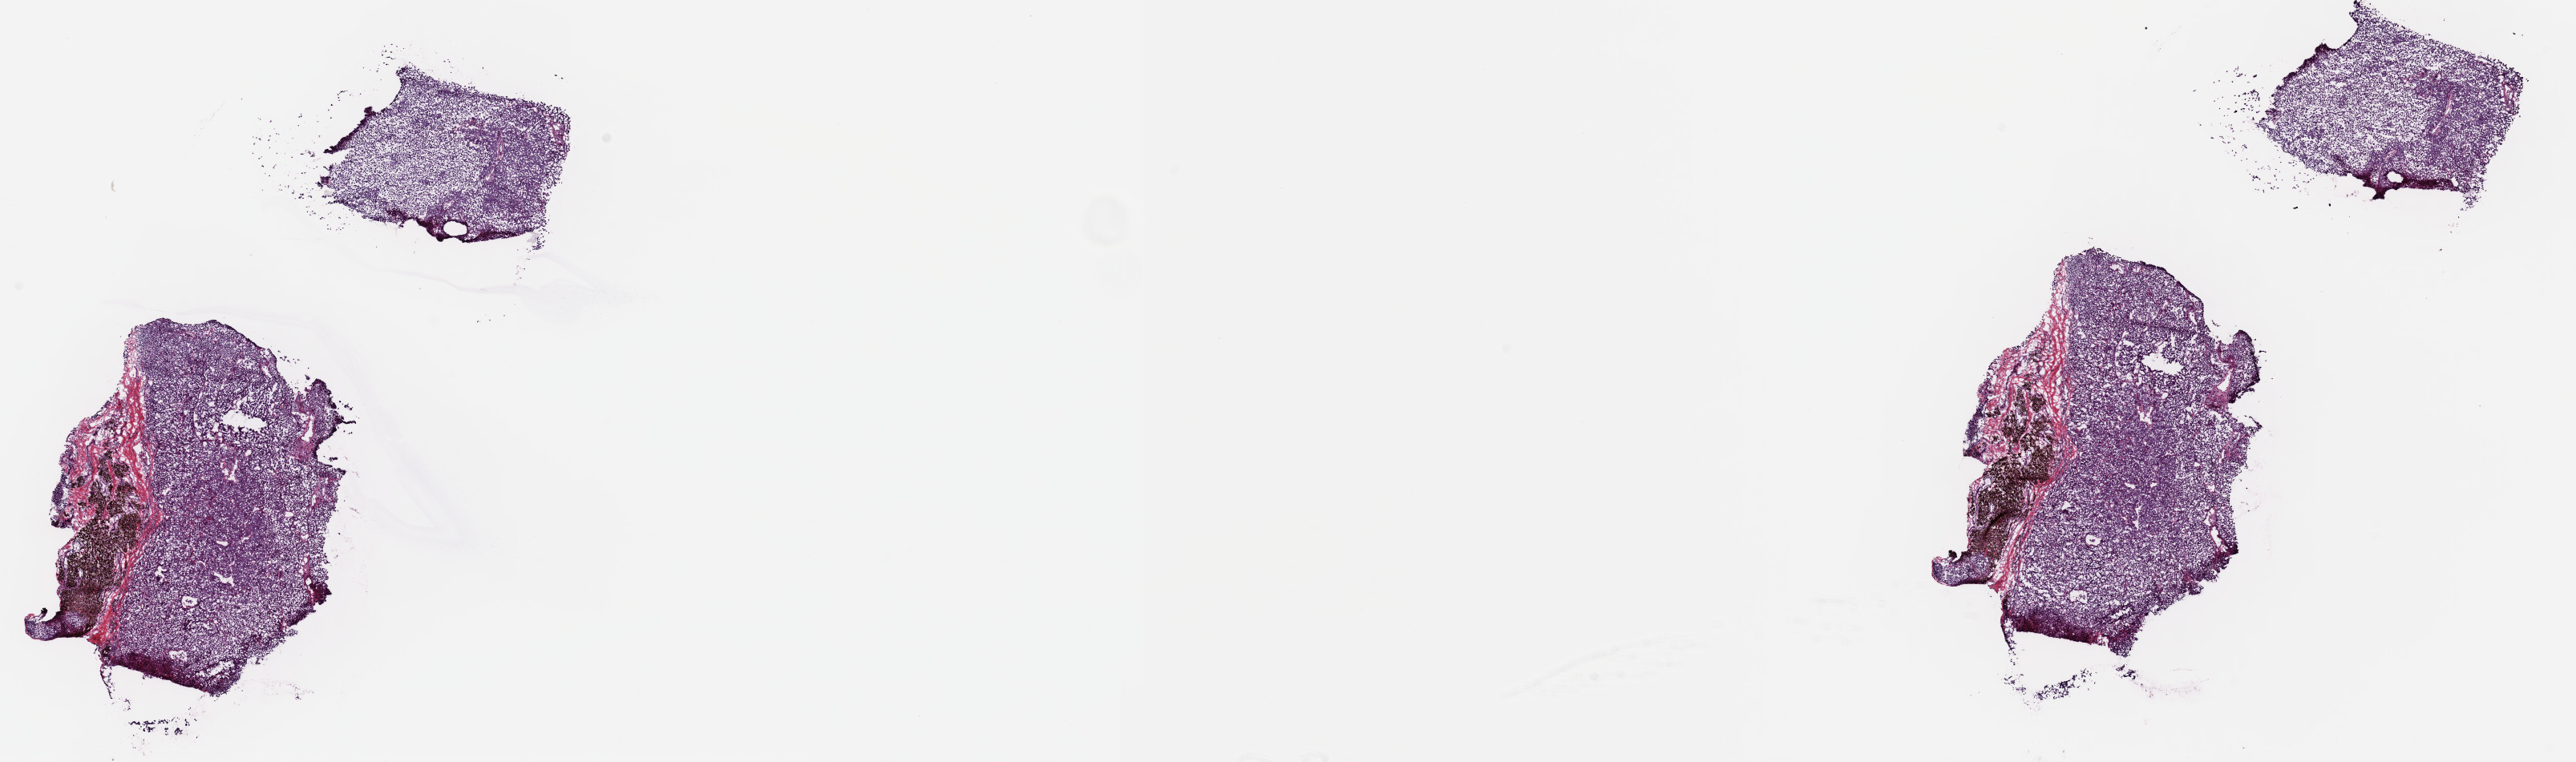
Digitized Hematoxylin and eosin (H&E) stained tissue section (whole slide), shown as a low-resolution overview of the whole scanned area (about 25.4 x 7.5 mm, from a 40x scan). Frozen section from the top of the tissue portion. Metastatic tumour sample. Patient: female, age at initial diagnosis 70 years. Pathologist review of this section (percent, as recorded): tumour cells 80%, tumour nuclei 90%, normal cells 0%, stromal cells 20%, necrosis 0%. Infiltration values recorded for this section: lymphocyte infiltration 0%, monocyte infiltration 0%, neutrophil infiltration 0%.
This section: metastatic tumour tissue. Patient diagnosis: Malignant melanoma, NOS.